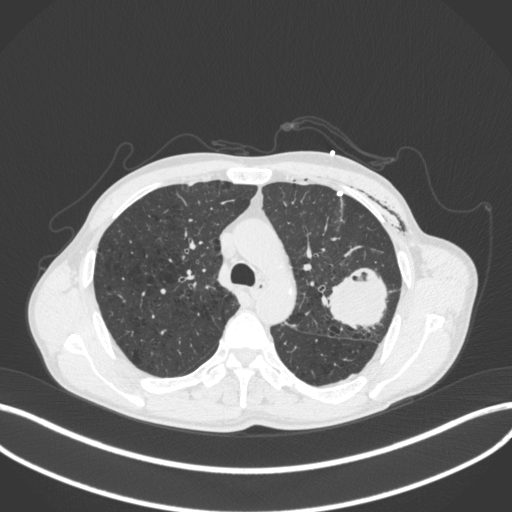
Chest CT, one axial slice. 120 kVp. Lung window (W 1500 / L -600 HU). 512 × 512 image matrix. Male patient, age 58 years. Case-level facts recorded for this patient, not image findings: clinical TNM (as recorded): T3 N0 M0.
Outlined on this slice (bounding box drawn by a radiologist):
- lung tumour (recorded histology: adenocarcinoma): bounding box [x1, y1, x2, y2] px = [319, 264, 393, 334]